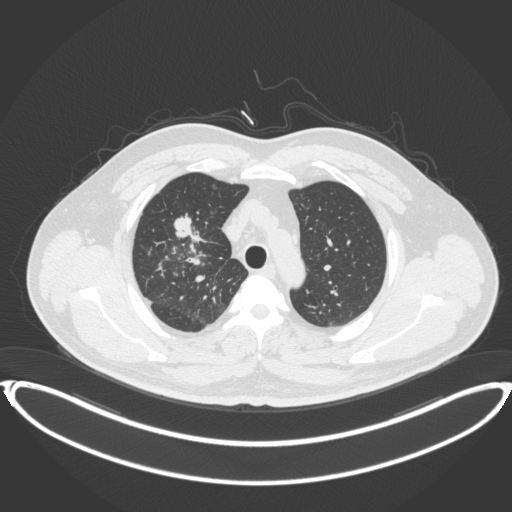
Chest CT, one axial slice. Slice 300 of 399 in the series (ordered by position). 120 kVp. Lung window (W 1500 / L -600 HU). 512 × 512 image matrix, field of view 445 × 445 mm. Male patient, age 53 years. Case-level facts recorded for this patient, not image findings: clinical TNM (as recorded): T2a N0 M0.
Outlined on this slice (rectangle marked by the reading radiologist):
- lung tumour (recorded histology: adenocarcinoma): bounding box (x1, y1, x2, y2) in pixels: (172, 213, 207, 249)